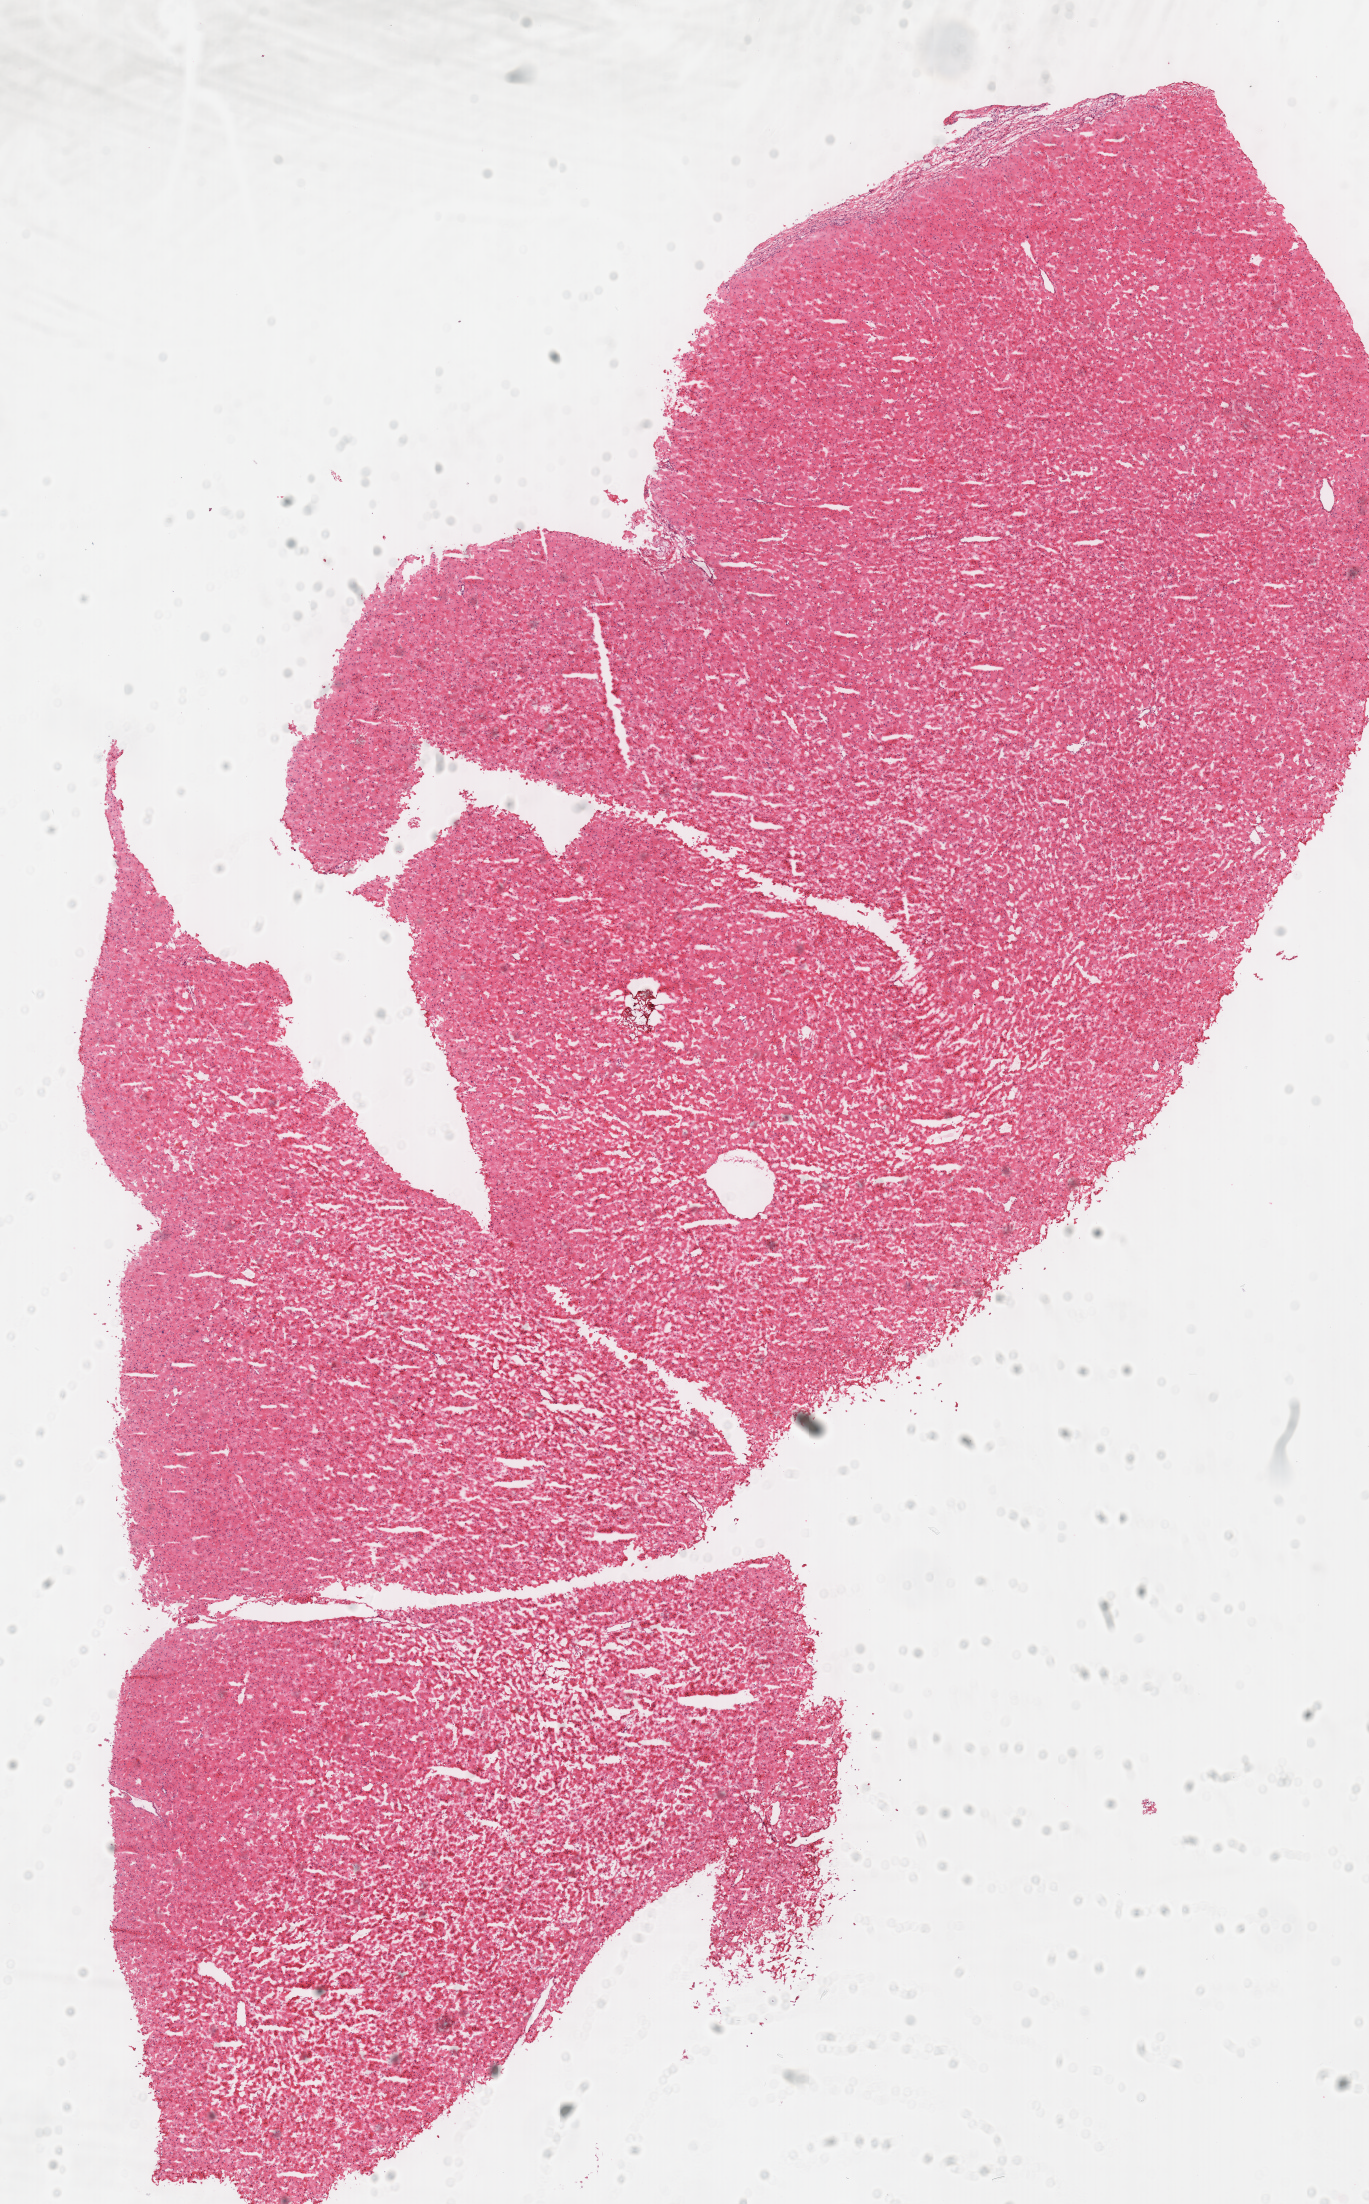
Digitized H&E-stained tissue section (whole slide), whole scanned area (about 10.8 x 17.3 mm, acquisition: 40x scan) shown as a low-resolution overview. Frozen section from the top of the tissue portion. Kidney, primary tumour sample. Female patient; age at initial diagnosis 42 years. Composition of this section per pathologist review: tumour cells 100%, tumour nuclei 95%, normal cells 0%, stromal cells 0%, necrosis 0%. Inflammatory infiltration, as recorded: lymphocyte infiltration 0%, monocyte infiltration 0%, neutrophil infiltration 0%.
AJCC pathologic stage: I. Pathologic diagnosis: Renal cell carcinoma, chromophobe type.